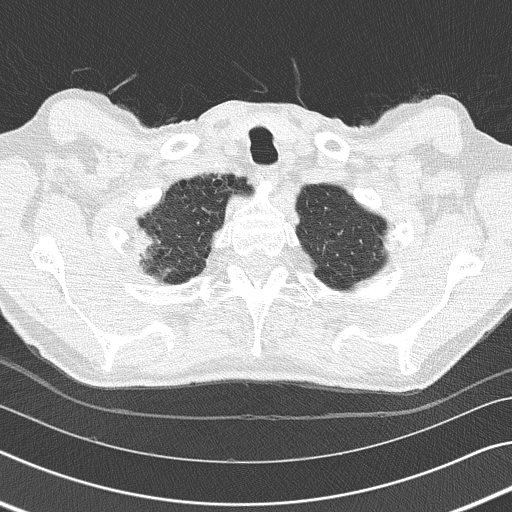
Low-dose screening chest CT, one axial slice. Slice 146 of 155 in the series (ordered by position). 120 kVp. Lung window (W 1500 / L -600 HU). 2 mm slice thickness. 512 × 512 image matrix.
Annotated regions visible in this slice (expert manual segmentation):
- lesion 1 (tumor, middle lobe of right lung): bounding box <137,228,158,261> (left, top, right, bottom; pixels)